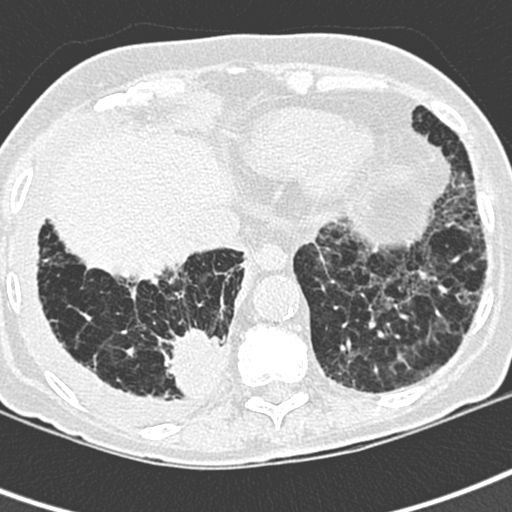
Low-dose screening chest CT, one axial slice; slice 71 of 220 in the series (ordered by position); 120 kVp; lung window (W 1500 / L -600 HU); 512 × 512 image matrix, field of view 288 × 288 mm.
Structures marked on this image (outlined manually by an expert reader):
- lesion 1 (tumor, lower lobe of right lung): bounding box (x1, y1, x2, y2) in pixels: (164, 328, 223, 398)